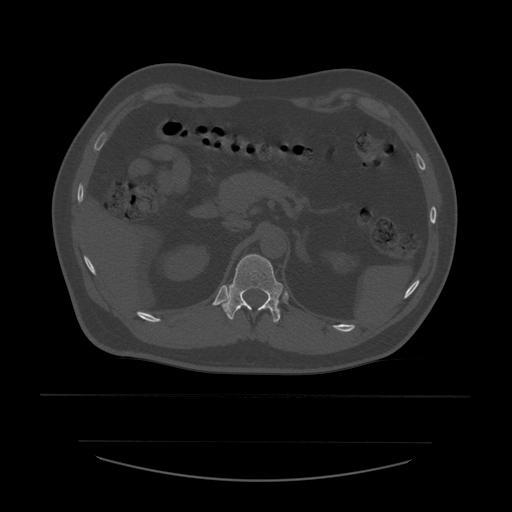
CT including the spine, one axial slice; position 255 of 532 along the scan axis; reconstruction kernel STANDARD; 120 kVp; bone window (W 1800 / L 400 HU); 1.25 mm slice thickness; 512 × 512 image matrix, field of view 441 × 441 mm. Patient age 44 years. From the clinical record (not read from this slice): primary cancer: soft tissue sarcoma.
Outlined on this slice (semi-automatic segmentation, software-assisted and operator-edited):
- T12 vertebra: bounding box [x1, y1, x2, y2] px = [223, 254, 284, 323]